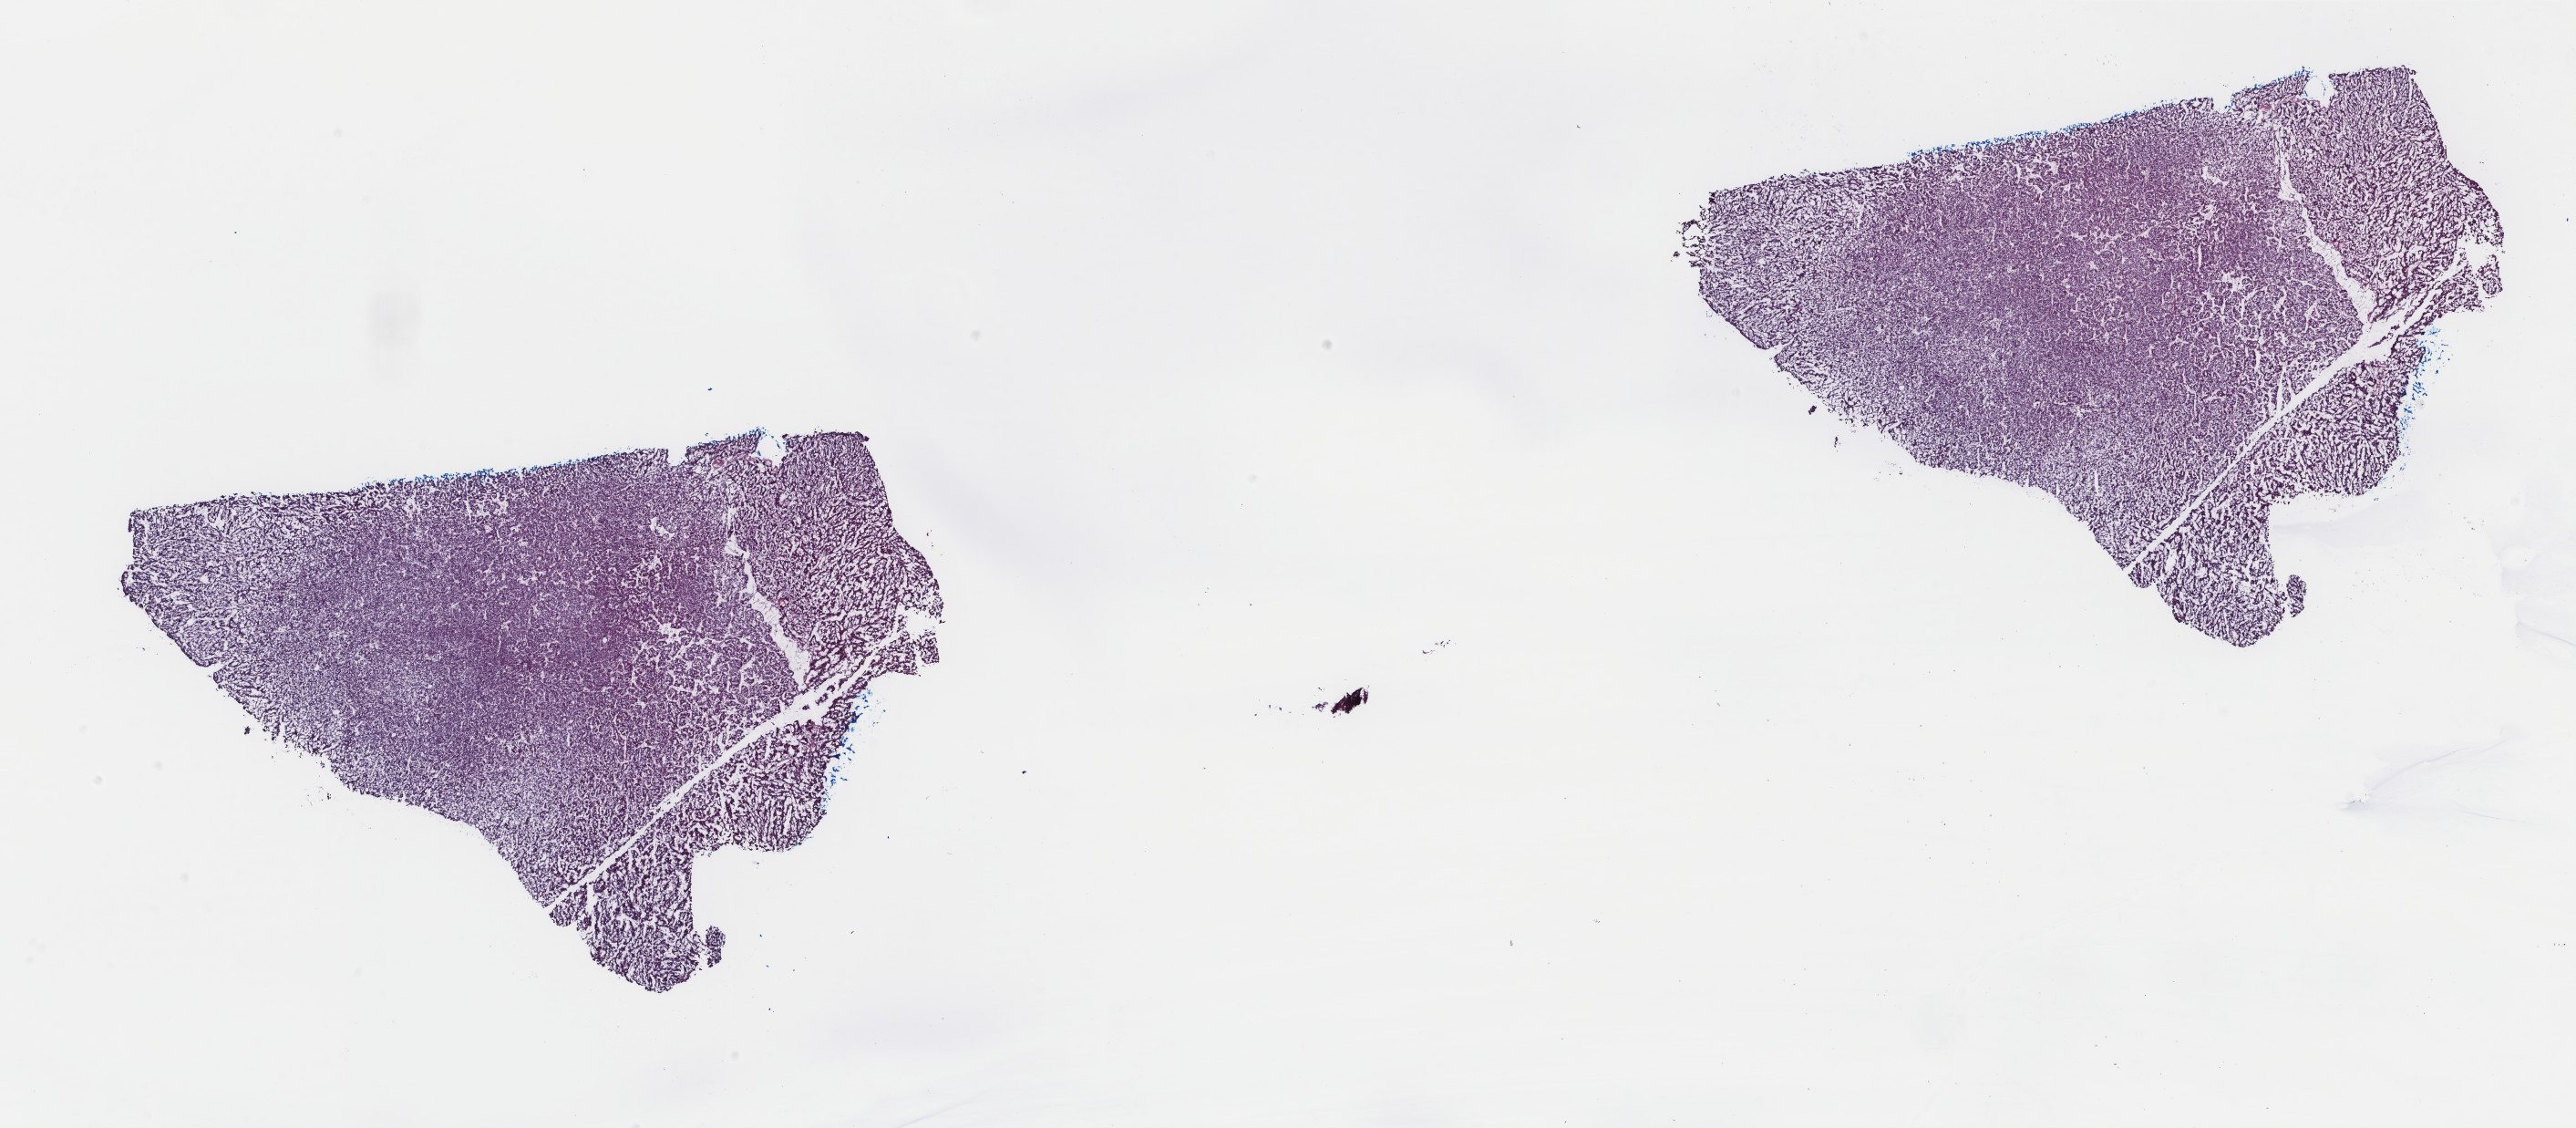
Hematoxylin and eosin (H&E) stained whole-slide image — a low-resolution overview of the entire scanned area, about 22.4 x 9.8 mm, frozen section from the top of the tissue portion, sample: primary tumour, liver. Male patient; age at initial diagnosis 75 years. Composition of this section per pathologist review: tumour cells 100%, tumour nuclei 95%, normal cells 0%, stromal cells 0%, necrosis 0%. Inflammatory infiltration, as recorded: lymphocyte infiltration 0%, monocyte infiltration 0%, neutrophil infiltration 0%.
- AJCC pathologic stage: I (6th edition)
- pathologic diagnosis: Hepatocellular carcinoma, NOS